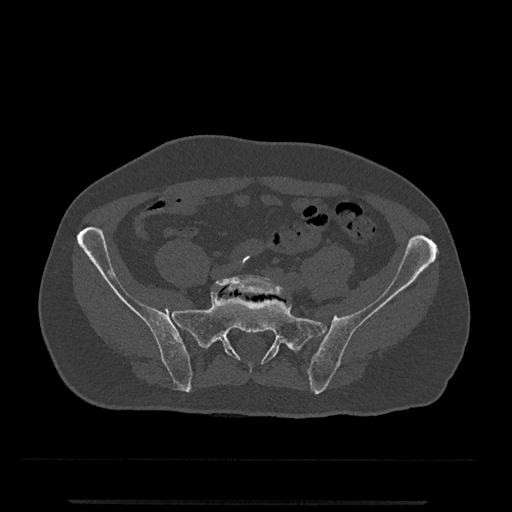
CT including the spine, one axial slice; position 22 of 797 along the scan axis; reconstruction kernel Br40s/3; bone window (W 1800 / L 400 HU); 0.5 mm slice thickness; 512 × 512 image matrix, field of view 419 × 419 mm. Male patient, age 63 years. Case-level facts recorded for this patient, not image findings: primary cancer: prostate.
Annotated regions visible in this slice (semi-automatic segmentation, software-assisted and operator-edited):
- L5 vertebra: bounding box [x1, y1, x2, y2] px = [214, 275, 284, 297]